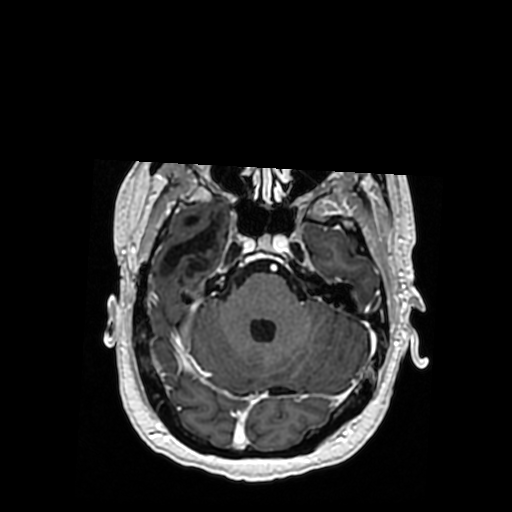
Brain MRI from a brain-tumour surgery series, one axial slice. Slice 247 of 364 in the series (ordered by position). T1-weighted post-contrast. 512 × 512 image matrix, field of view 260 × 260 mm. From the clinical record (not read from this slice): histopathology: Oligodendroglioma; WHO grade: 3; IDH mutation: yes; tumour location: Right Posterior Temporal Inferior Parietal.
Annotated regions visible in this slice (manually delineated by an expert):
- previous resection cavity: bounding box <161,215,219,276> (left, top, right, bottom; pixels)